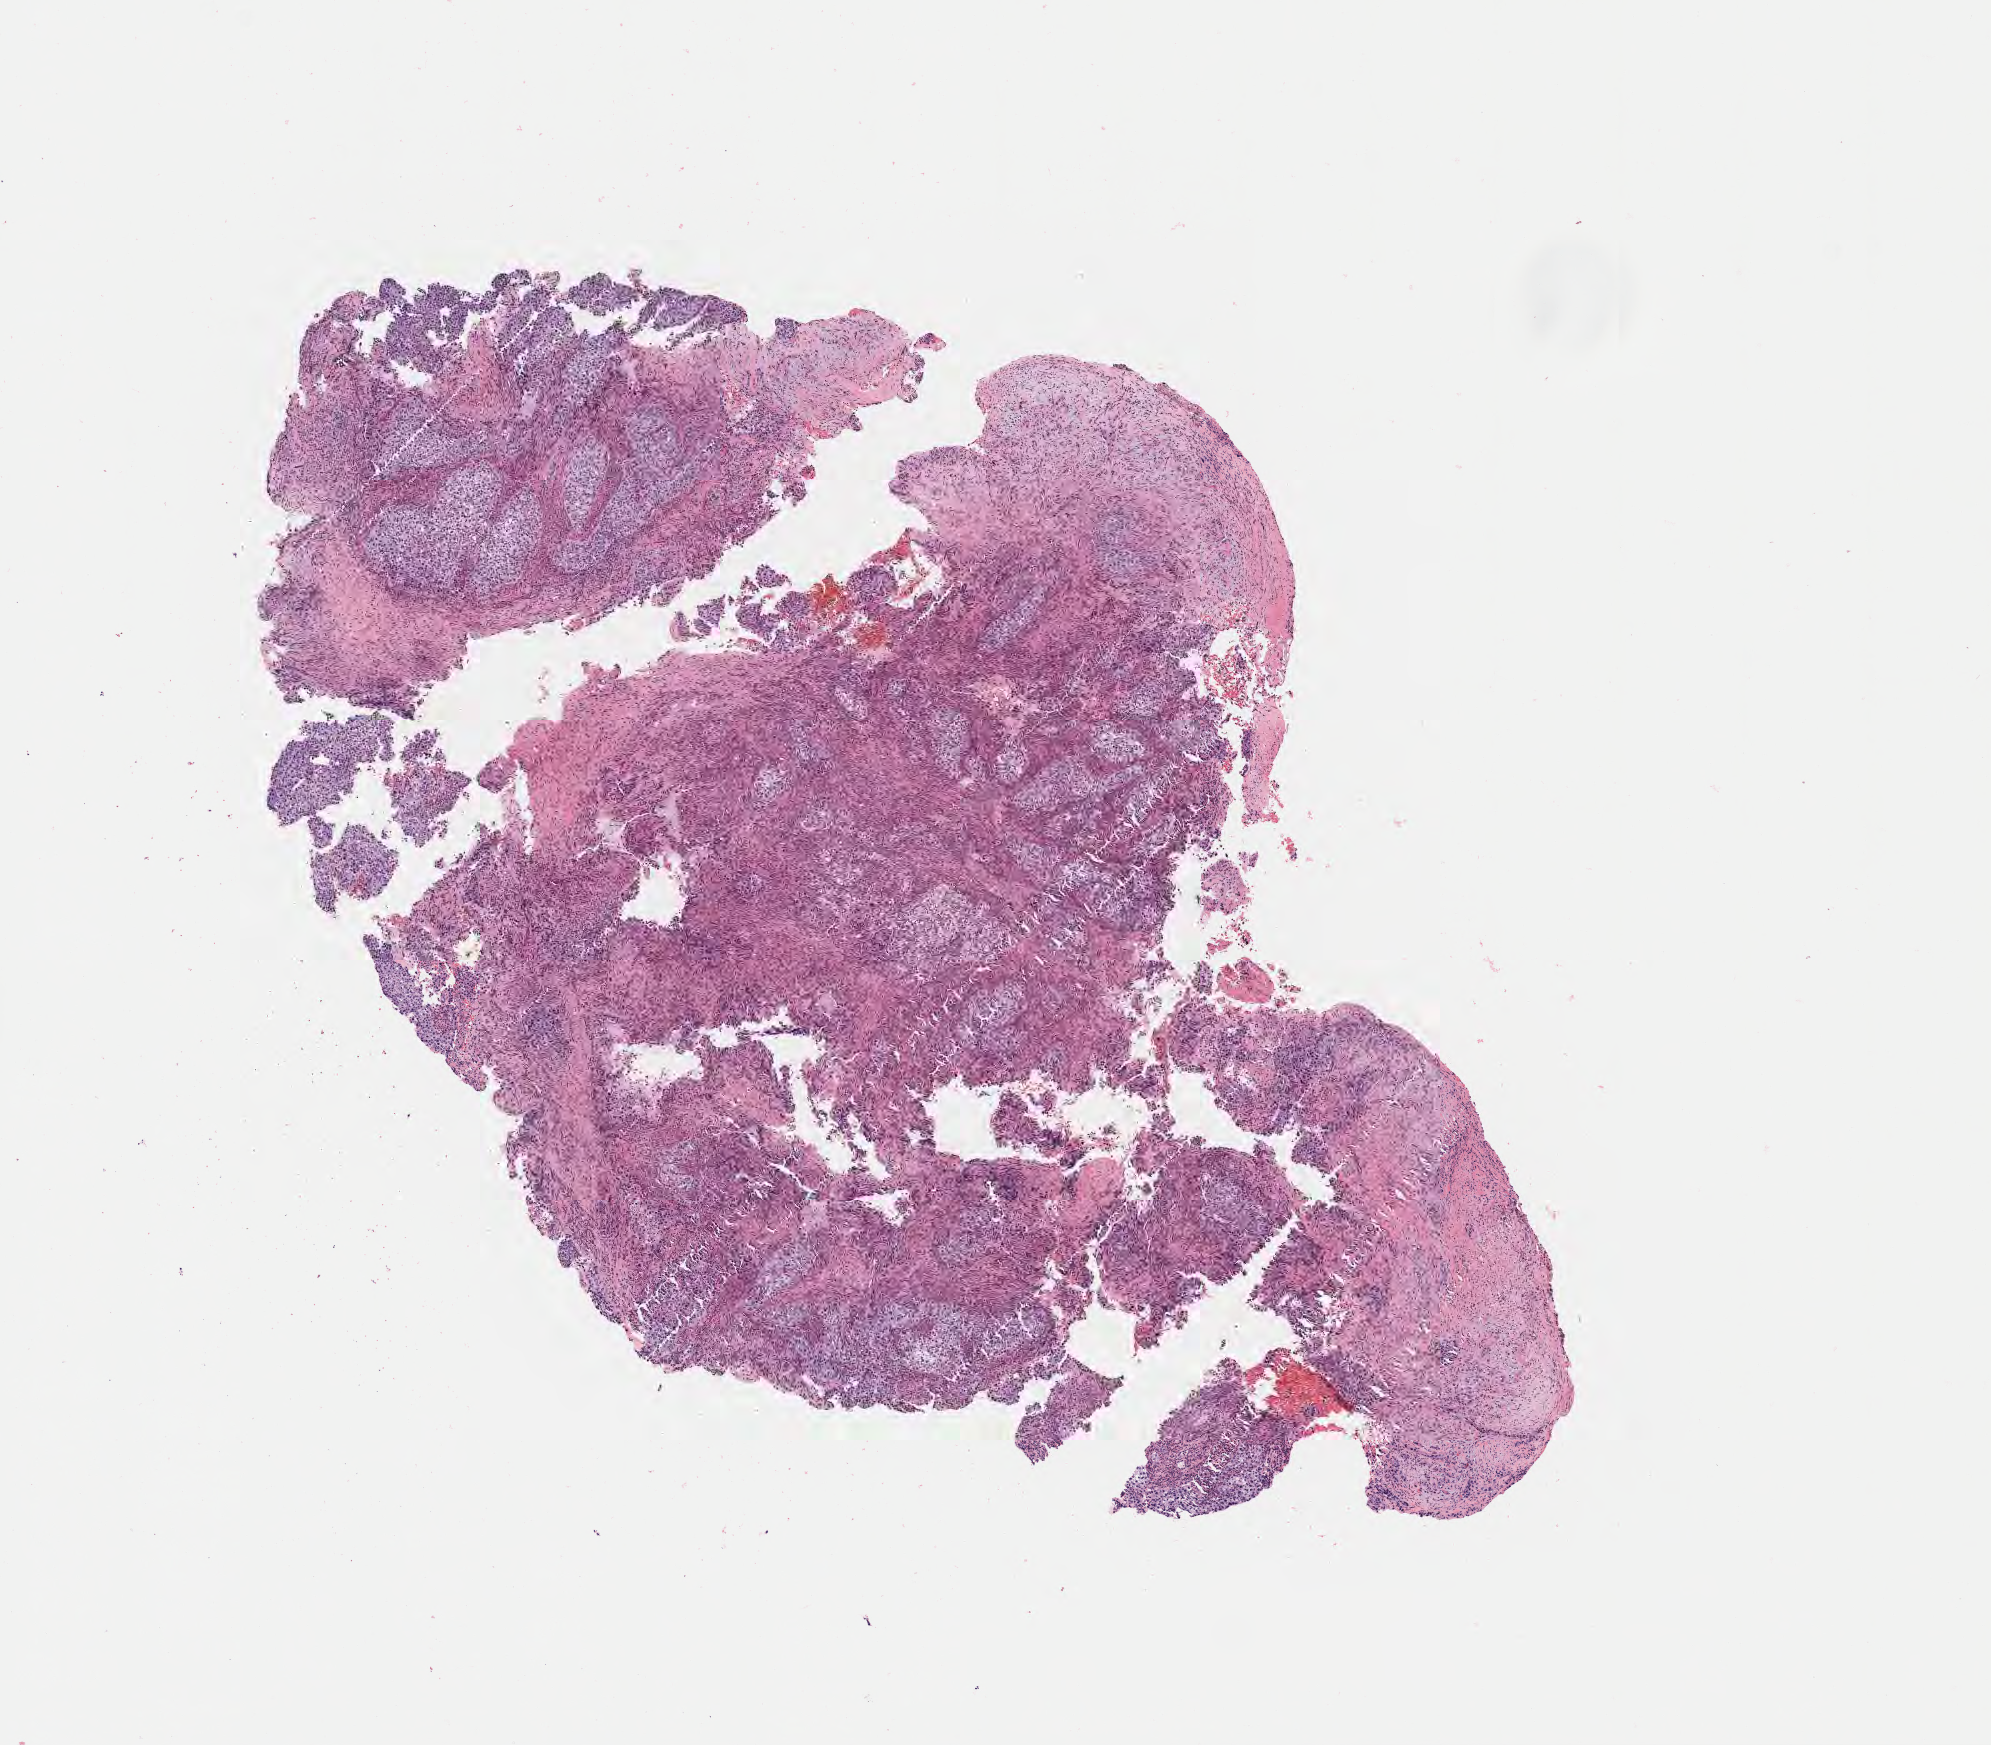
Haematoxylin and eosin whole-slide image — a low-resolution overview of the entire scanned area, about 8.1 x 7.1 mm. Specimen: tumor tissue. Site: cervix. Patient: female, aged 39.
Diagnosis: Squamous cell carcinoma, large cell, nonkeratinizing, NOS.